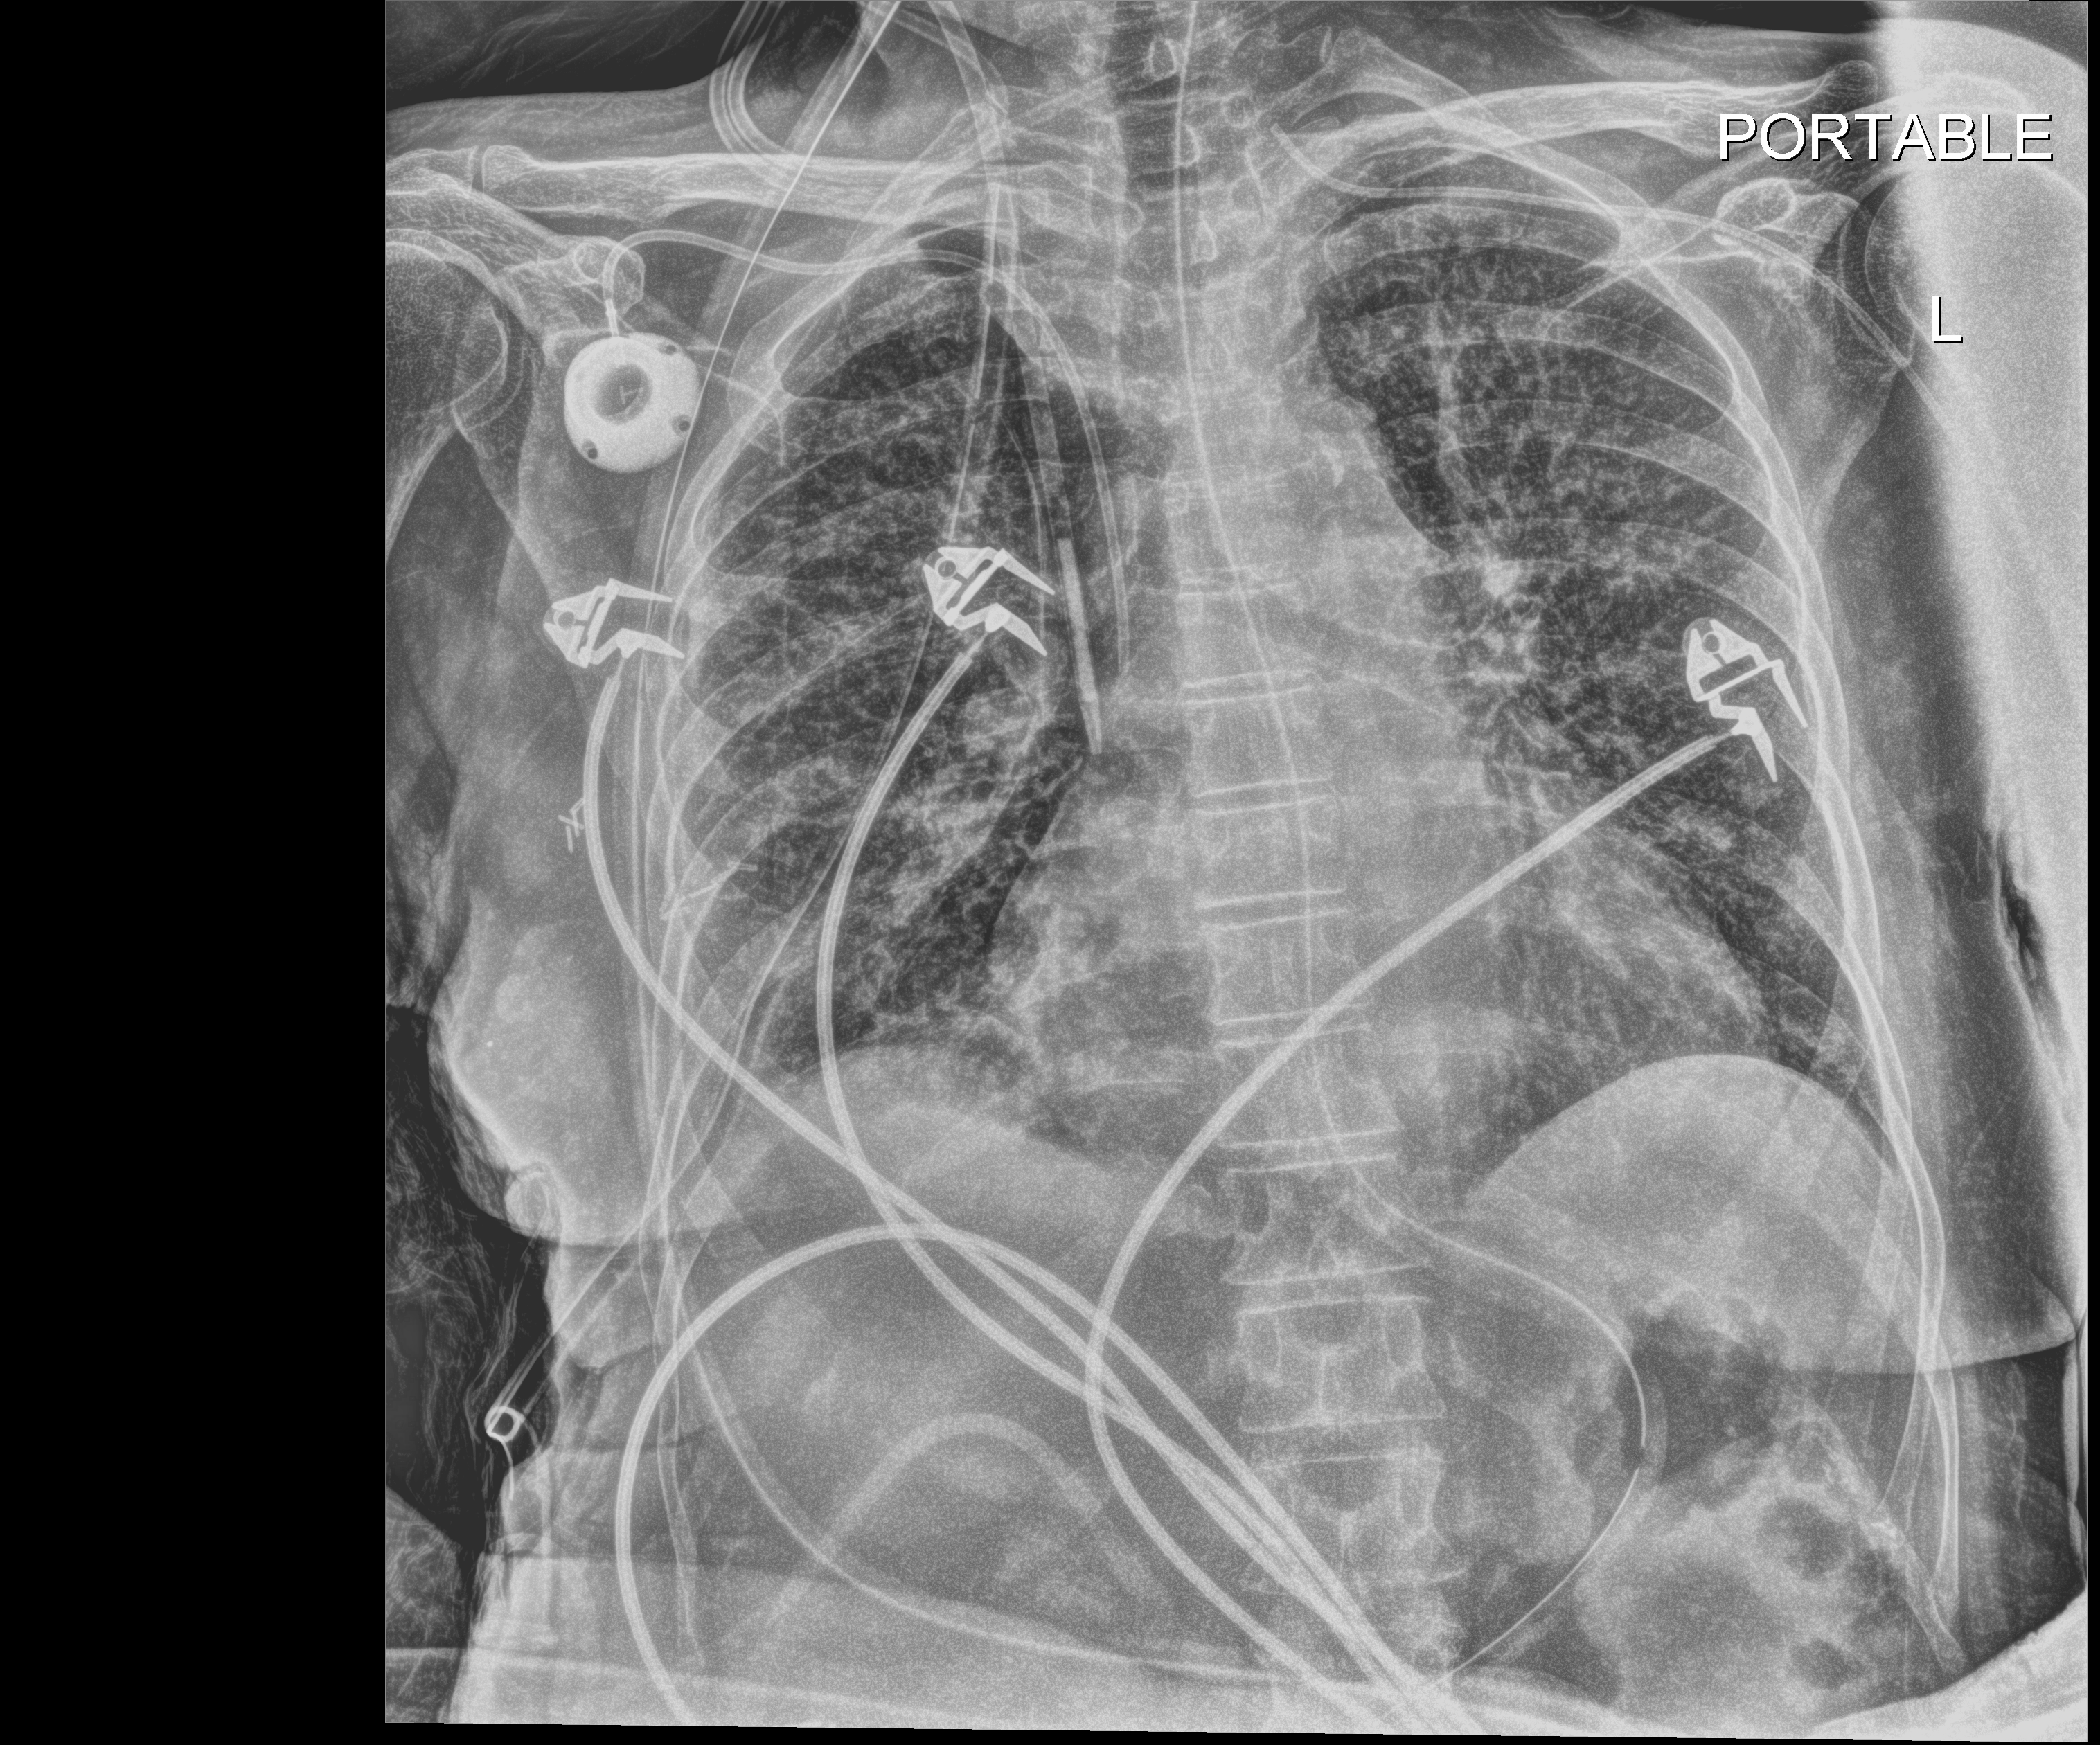
Chest X-ray (portable). Patient hospitalised with COVID-19; female, aged 60–74 years.
From the hospital-stay record, not from the radiograph (when in the stay this image was taken is not recorded):
- mechanically ventilated during this hospital stay: yes